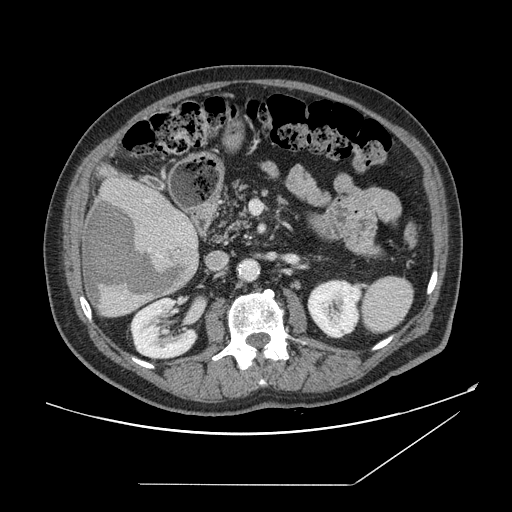
Contrast-enhanced abdominal CT, one axial slice; position 70 of 166 along the scan axis; soft-tissue window (W 400 / L 40 HU); 2.5 mm slice thickness; 512 × 512 image matrix, field of view 416 × 416 mm. Male patient, age 80 years. From the clinical record (not read from this slice): diagnosis: colorectal cancer liver metastases, imaged before liver resection; multiple liver metastases: no; largest metastasis: 2.2 cm; disease in both lobes: no.
Annotated regions visible in this slice (expert manual segmentation):
- liver: box from (x=81, y=176) to (x=199, y=318) px
- planned liver remnant (the part of the liver to remain after resection): (x=108, y=175)–(x=182, y=217)
- liver metastasis: (x=84, y=199)–(x=181, y=308)